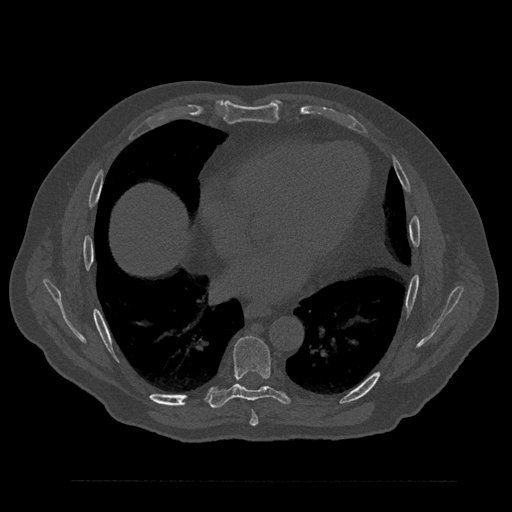
CT including the spine, one axial slice. Position 458 of 797 along the scan axis. Reconstruction kernel Br40s/3. Bone window (W 1800 / L 400 HU). 512 × 512 image matrix, field of view 430 × 430 mm. Male patient, age 61 years. Case-level facts recorded for this patient, not image findings: primary cancer: prostate.
Annotated regions visible in this slice (semi-automatic segmentation, software-assisted and operator-edited):
- T7 vertebra: box from (x=250, y=411) to (x=259, y=426) px
- T8 vertebra: (x=208, y=336)–(x=290, y=409)